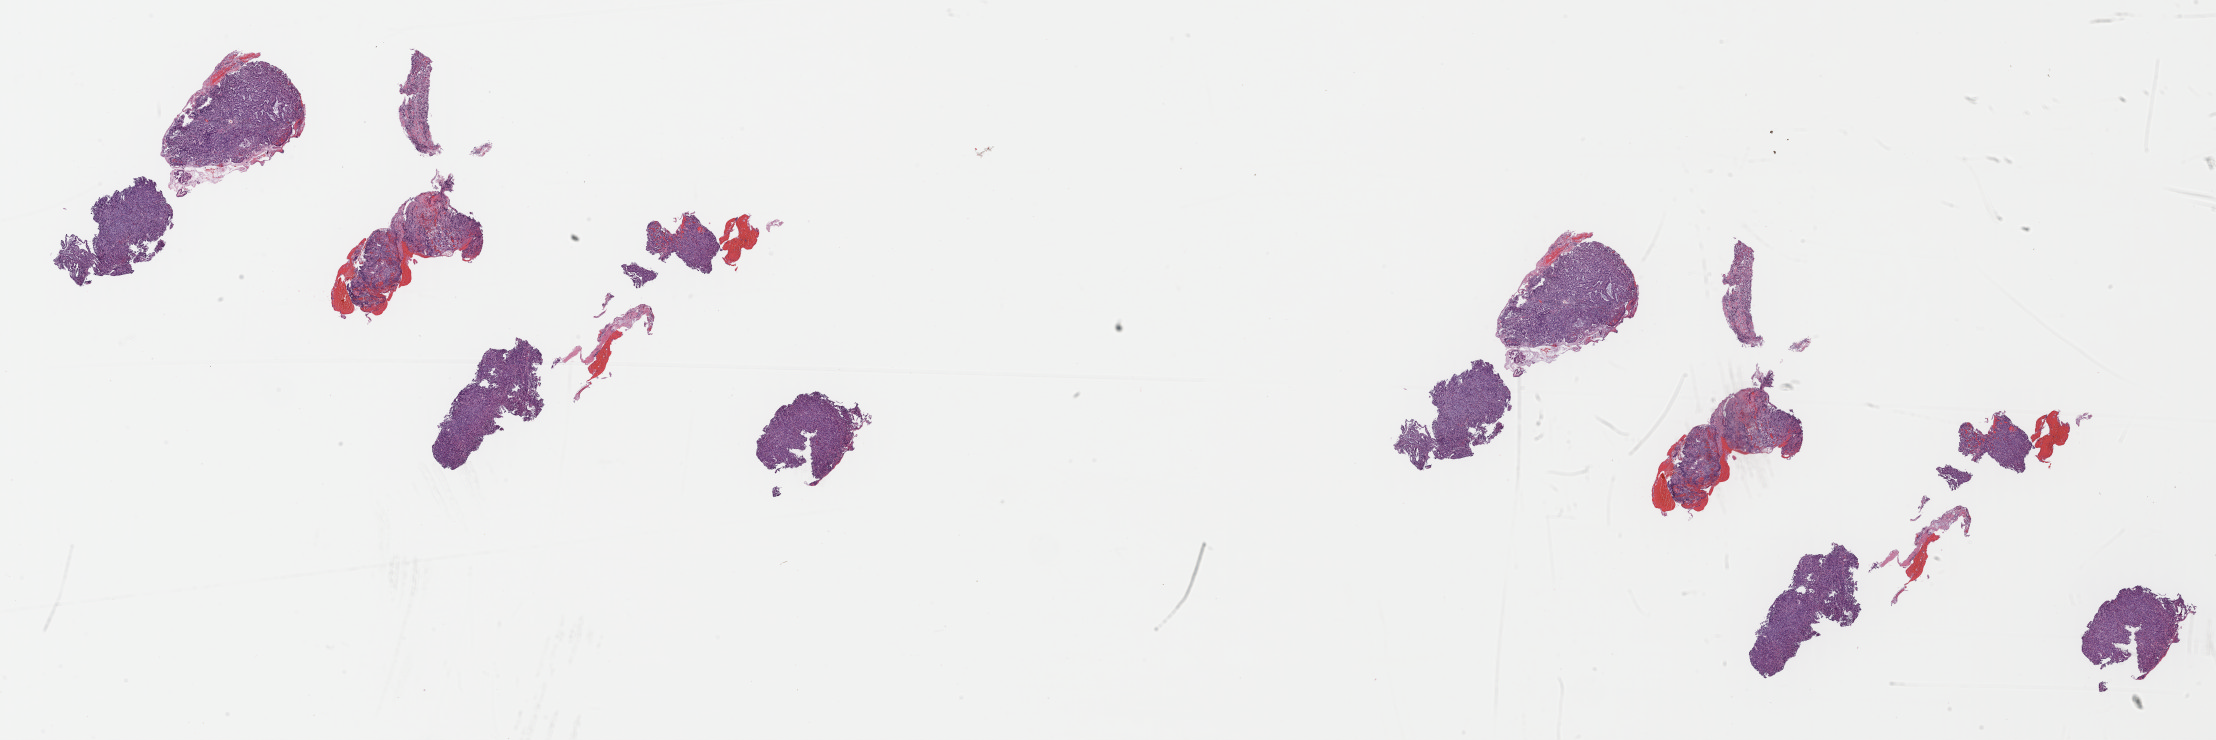
H&E-stained whole-slide image — shown as a low-resolution overview of the whole scanned area (about 35.0 x 11.7 mm); FFPE section; sample: primary tumour, esophagus. Female patient; age at initial diagnosis 74 years. Histologic grade: G3 (poorly differentiated). Composition of this section per pathologist review: tumour cells 80%, tumour nuclei 80%, normal cells 0%, stromal cells 20%, necrosis 0%. Infiltration values recorded for this section: lymphocyte infiltration 40%, monocyte infiltration 20%, neutrophil infiltration 20%.
Pathologic diagnosis: Adenocarcinoma, NOS (lower third of esophagus).